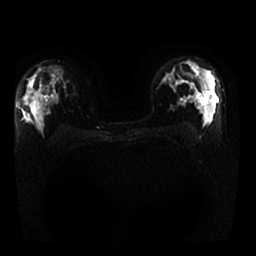
Breast MRI, one axial slice; position 15 of 25 along the scan axis; diffusion-weighted series; image 2 of 4 stored at this slice position (different b-values; order by instance number); 1.5 T; 4 mm slice thickness; 256 × 256 image matrix, field of view 340 × 340 mm. Female patient.
Annotated regions visible in this slice (expert manual segmentation):
- tumour on diffusion-weighted imaging: bounding box (x1, y1, x2, y2) in pixels: (28, 88, 35, 96)